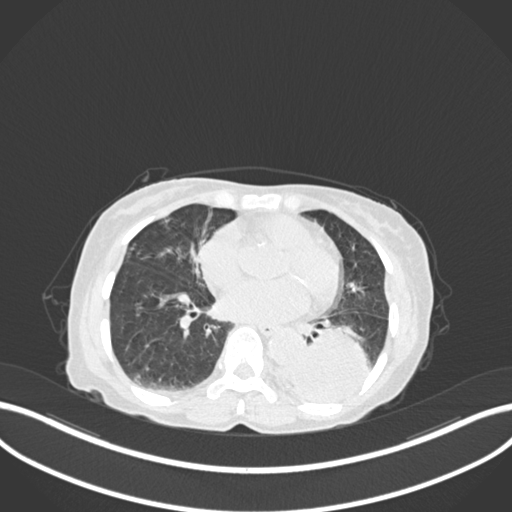
Chest CT, one axial slice. Position 57 of 233 along the scan axis. Reconstruction kernel B30f. 120 kVp. Lung window (W 1500 / L -600 HU). 1 mm slice thickness. 512 × 512 image matrix, field of view 400 × 400 mm. Patient: female, 78 years. Case-level facts recorded for this patient, not image findings: clinical TNM (as recorded): T3 N0 M1.
Outlined on this slice (bounding box drawn by a radiologist):
- lung tumour (recorded histology: squamous cell carcinoma): box from (x=289, y=327) to (x=376, y=407) px